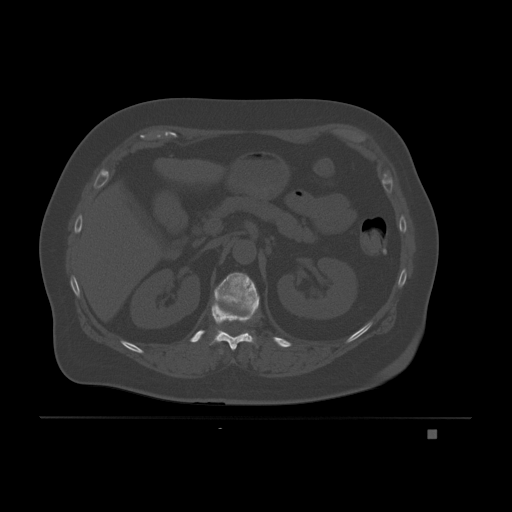
CT including the spine, one axial slice. Position 87 of 221 along the scan axis. Bone window (W 1800 / L 400 HU). 3 mm slice thickness. 512 × 512 image matrix, field of view 474 × 474 mm. Patient: female, 63 years. From the clinical record (not read from this slice): primary cancer: breast.
Structures marked on this image (semi-automatically segmented with operator editing):
- T11 vertebra: bounding box [x1, y1, x2, y2] px = [210, 304, 257, 350]
- T12 vertebra: [213, 272, 260, 313]